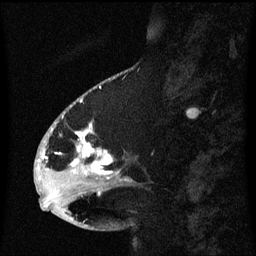
Breast MRI (dynamic contrast-enhanced), one sagittal slice. Slice 24 of 60 in the series (ordered by position). Dynamic contrast-enhanced series, image 2 of 3 at this slice position (ordered by acquisition). 1.5 T. TE 4.2 ms, TR 8.4 ms. 2.1 mm slice thickness. 256 × 256 image matrix. Patient: female, 53 years. Case-level facts recorded for this patient, not image findings: setting: breast cancer imaged before/during neoadjuvant chemotherapy; receptor status: HR-positive, HER2-negative.
Annotated regions visible in this slice (semi-automatically segmented with operator editing):
- analysis volume of interest (the breast-tissue region the enhancement analysis was run in; not a lesion): bounding box <49,108,133,201> (left, top, right, bottom; pixels)
- tumour enhancement mask (voxels above the 70 % enhancement threshold inside the analysis volume of interest): <72,124,114,175>